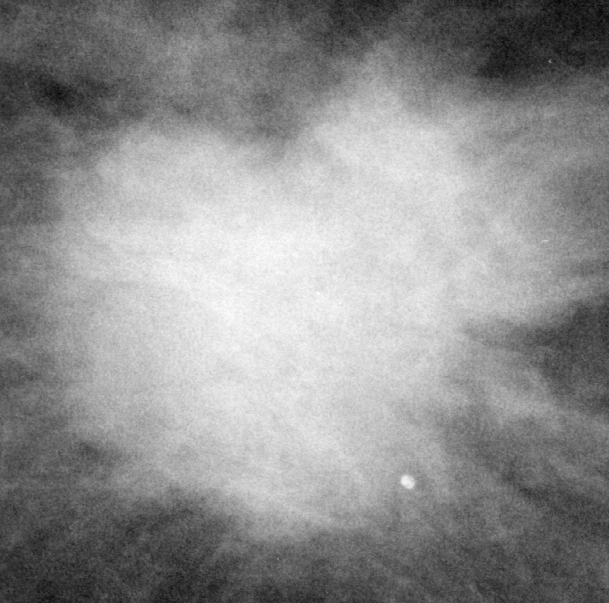
Cropped region of a digitized screen-film mammogram centred on a radiologist-marked abnormality, left breast, CC view.
Marked abnormality: mass, shape round / irregular / architectural distortion, margins spiculated; BI-RADS assessment category 5; subtlety rating 5 on a 1 (subtle) to 5 (obvious) scale; pathology result (as recorded, not read from the image): malignant.